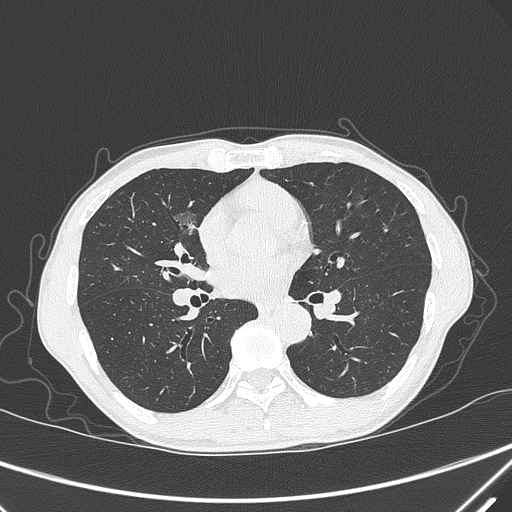
Chest CT, one axial slice. Position 168 of 339 along the scan axis. 120 kVp. Lung window (W 1500 / L -600 HU). 1 mm slice thickness. 512 × 512 image matrix. Male patient, age 67 years. From the clinical record (not read from this slice): clinical TNM (as recorded): T1c N0 M0.
Annotated regions visible in this slice (rectangle marked by the reading radiologist):
- lung tumour (recorded histology: adenocarcinoma): box from (x=166, y=204) to (x=205, y=247) px